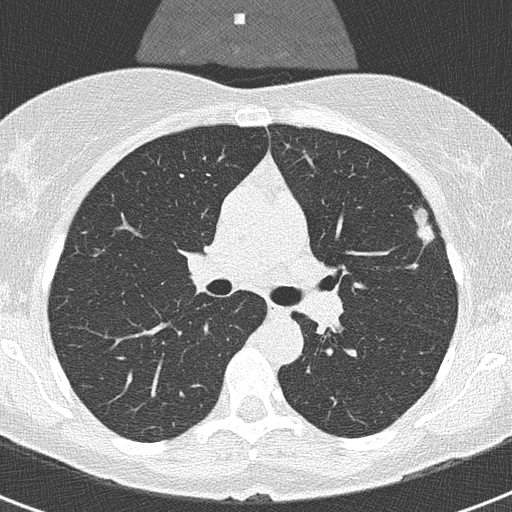
Low-dose screening chest CT, one axial slice; slice 207 of 320 in the series (ordered by position); lung window (W 1500 / L -600 HU); 2 mm slice thickness; 512 × 512 image matrix, field of view 290 × 290 mm.
Structures marked on this image (manually delineated by an expert):
- lesion 1 (tumor, upper lobe of left lung): bounding box <414,208,434,243> (left, top, right, bottom; pixels)